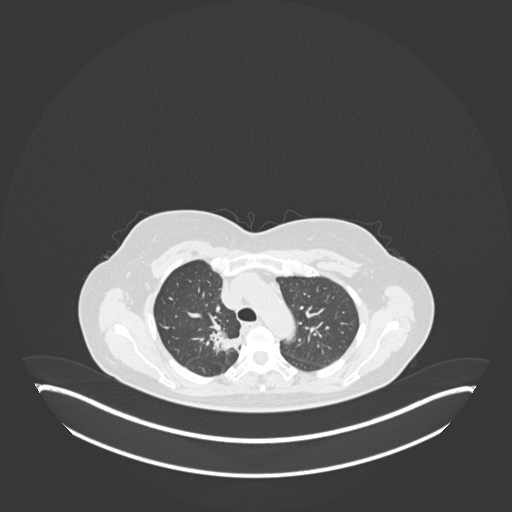
Chest CT, one axial slice. Slice 131 of 181 in the series (ordered by position). 120 kVp. Lung window (W 1500 / L -600 HU). 1 mm slice thickness. 512 × 512 image matrix. Patient: female, 65 years. Case-level facts recorded for this patient, not image findings: clinical TNM (as recorded): T1b N0 M0.
Structures marked on this image (rectangle marked by the reading radiologist):
- lung tumour (recorded histology: adenocarcinoma): box from (x=211, y=328) to (x=243, y=354) px